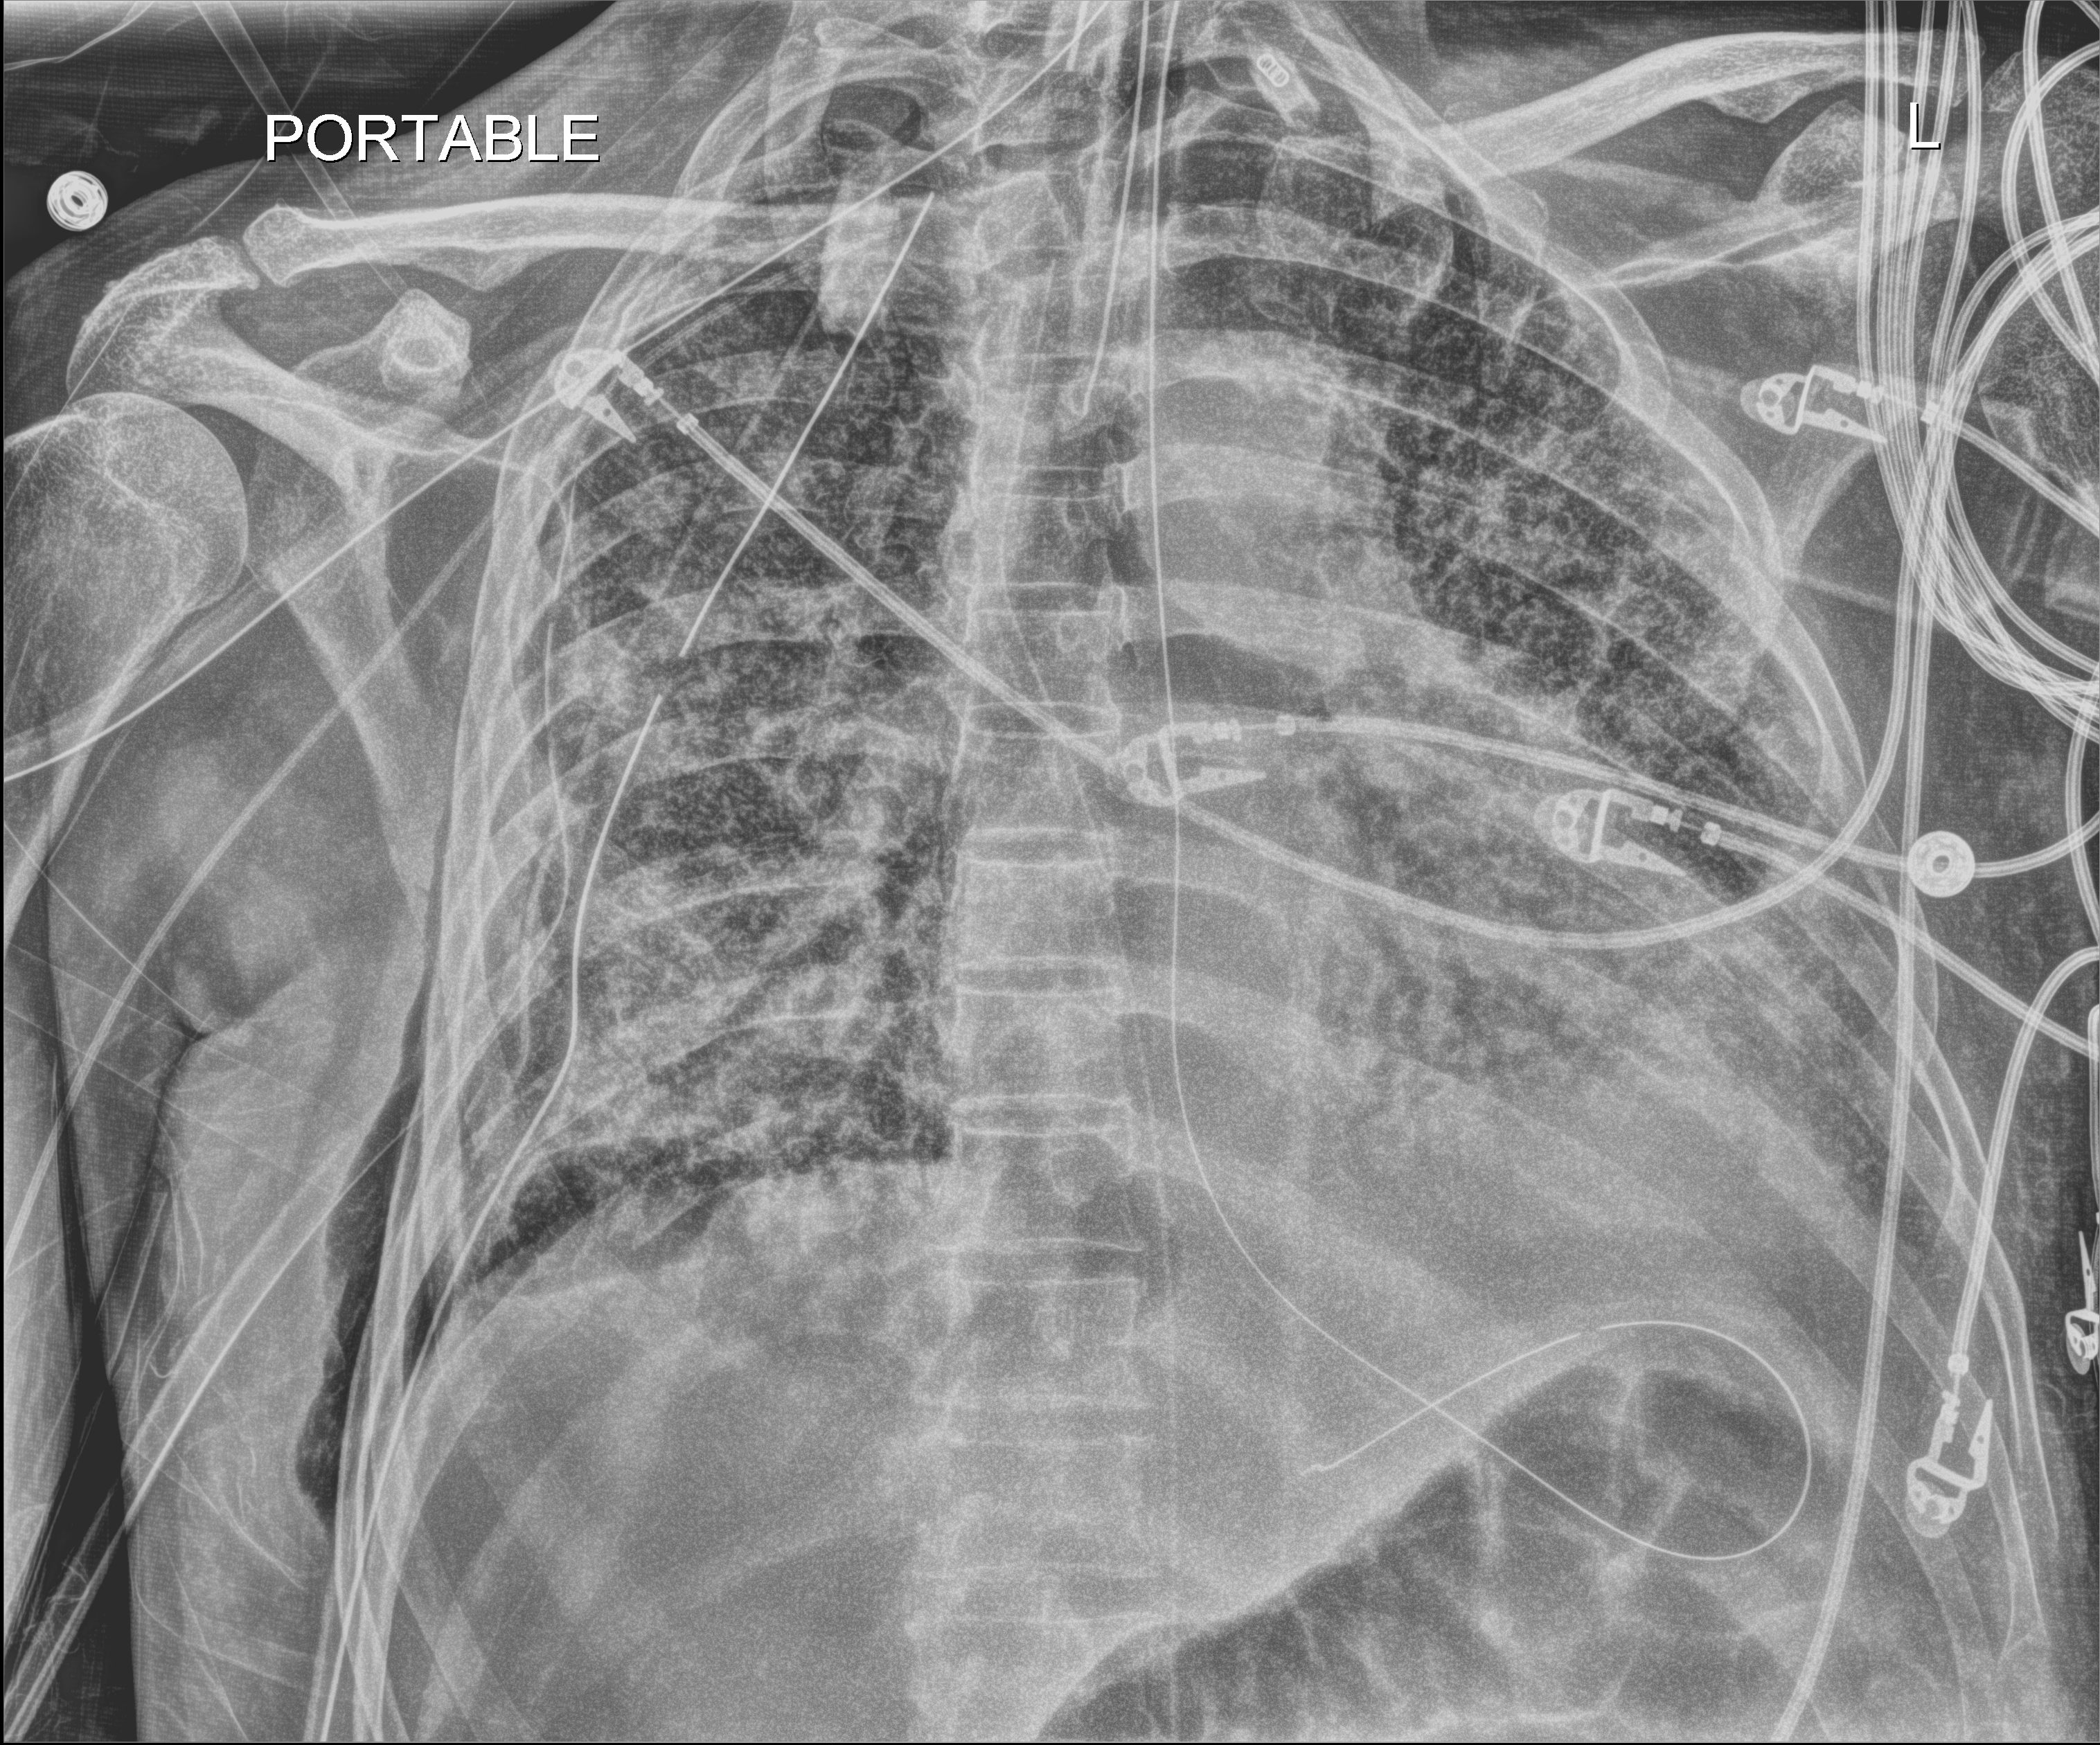
Bedside chest radiograph (digital radiography), anteroposterior (AP) projection. Patient hospitalised with COVID-19; male, aged 60–74 years.
Hospital-stay facts (about this admission, not read from this image; timing relative to this image not recorded): admitted to intensive care during this hospital stay: yes; mechanically ventilated during this hospital stay: yes; hypertension (admission record): yes.